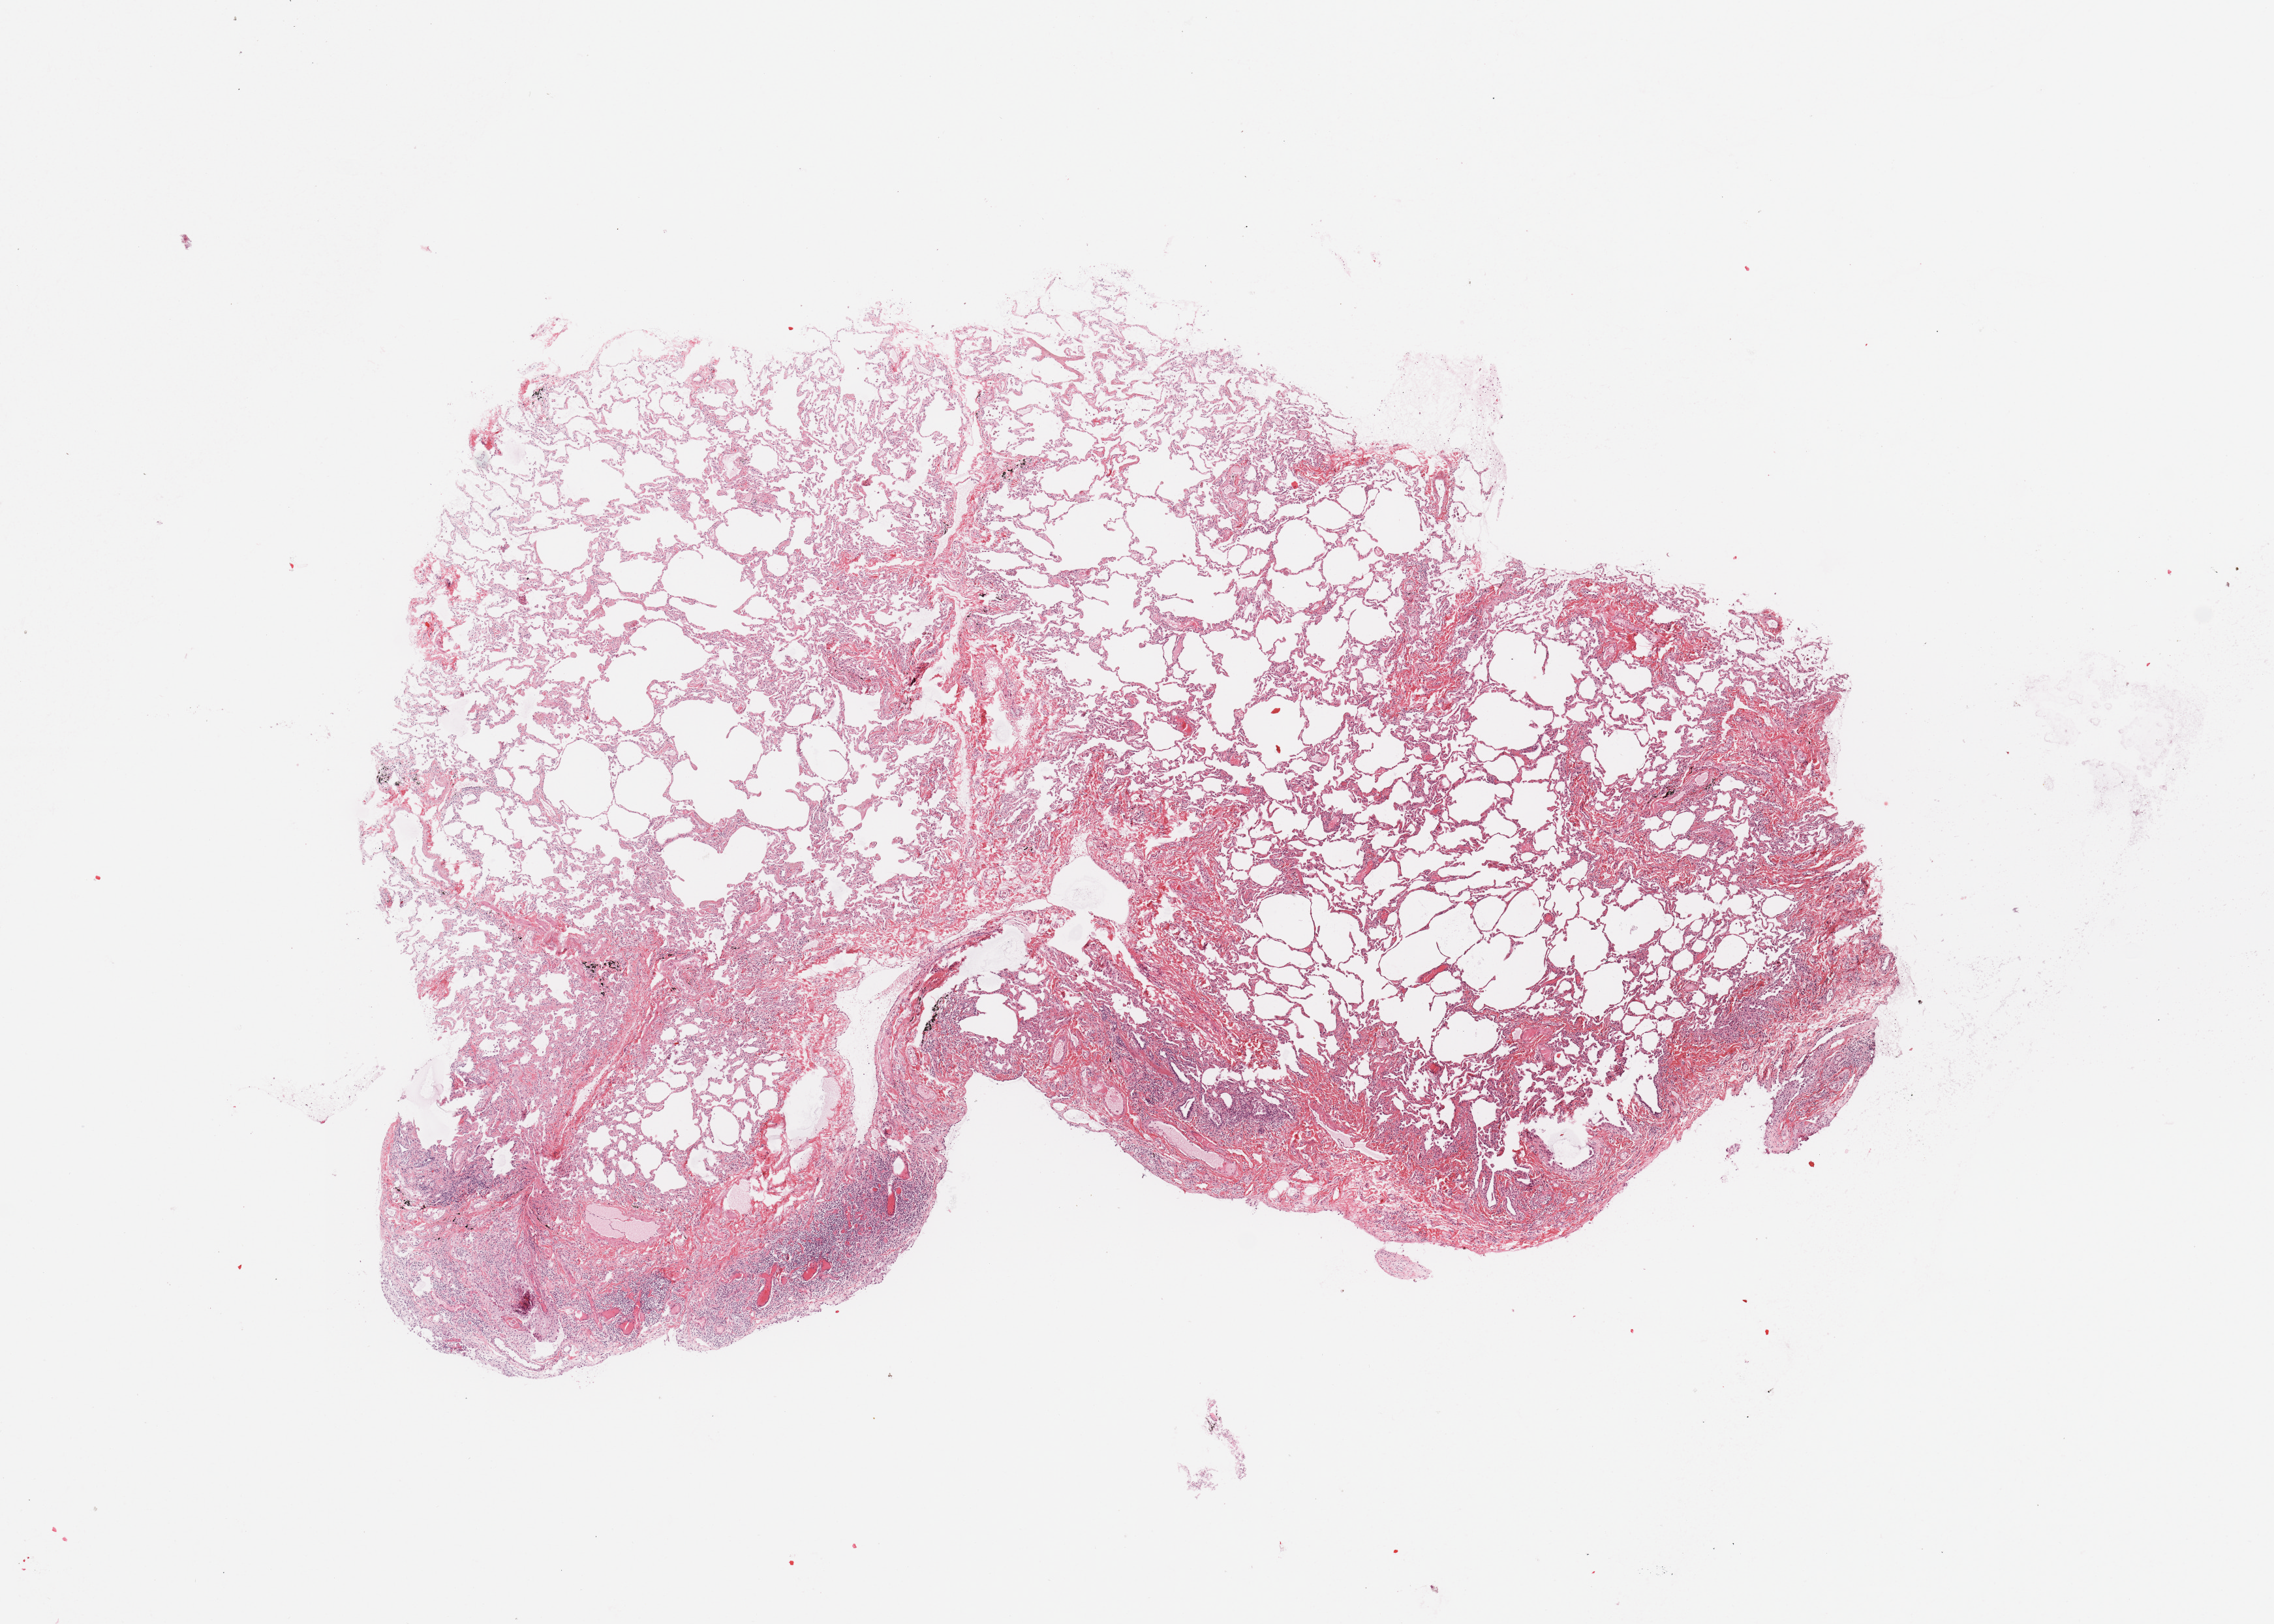
Digitized Hematoxylin and eosin (H&E) stained tissue section (whole slide) — low-resolution overview of the scanned area, about 13.8 x 9.8 mm (from a 20x scan), normal (non-tumour) tissue sample, sampled site: lung. Patient: male, age 63 years.
This section: normal (non-tumour) tissue from the same patient. Patient diagnosis: Squamous cell carcinoma, NOS.